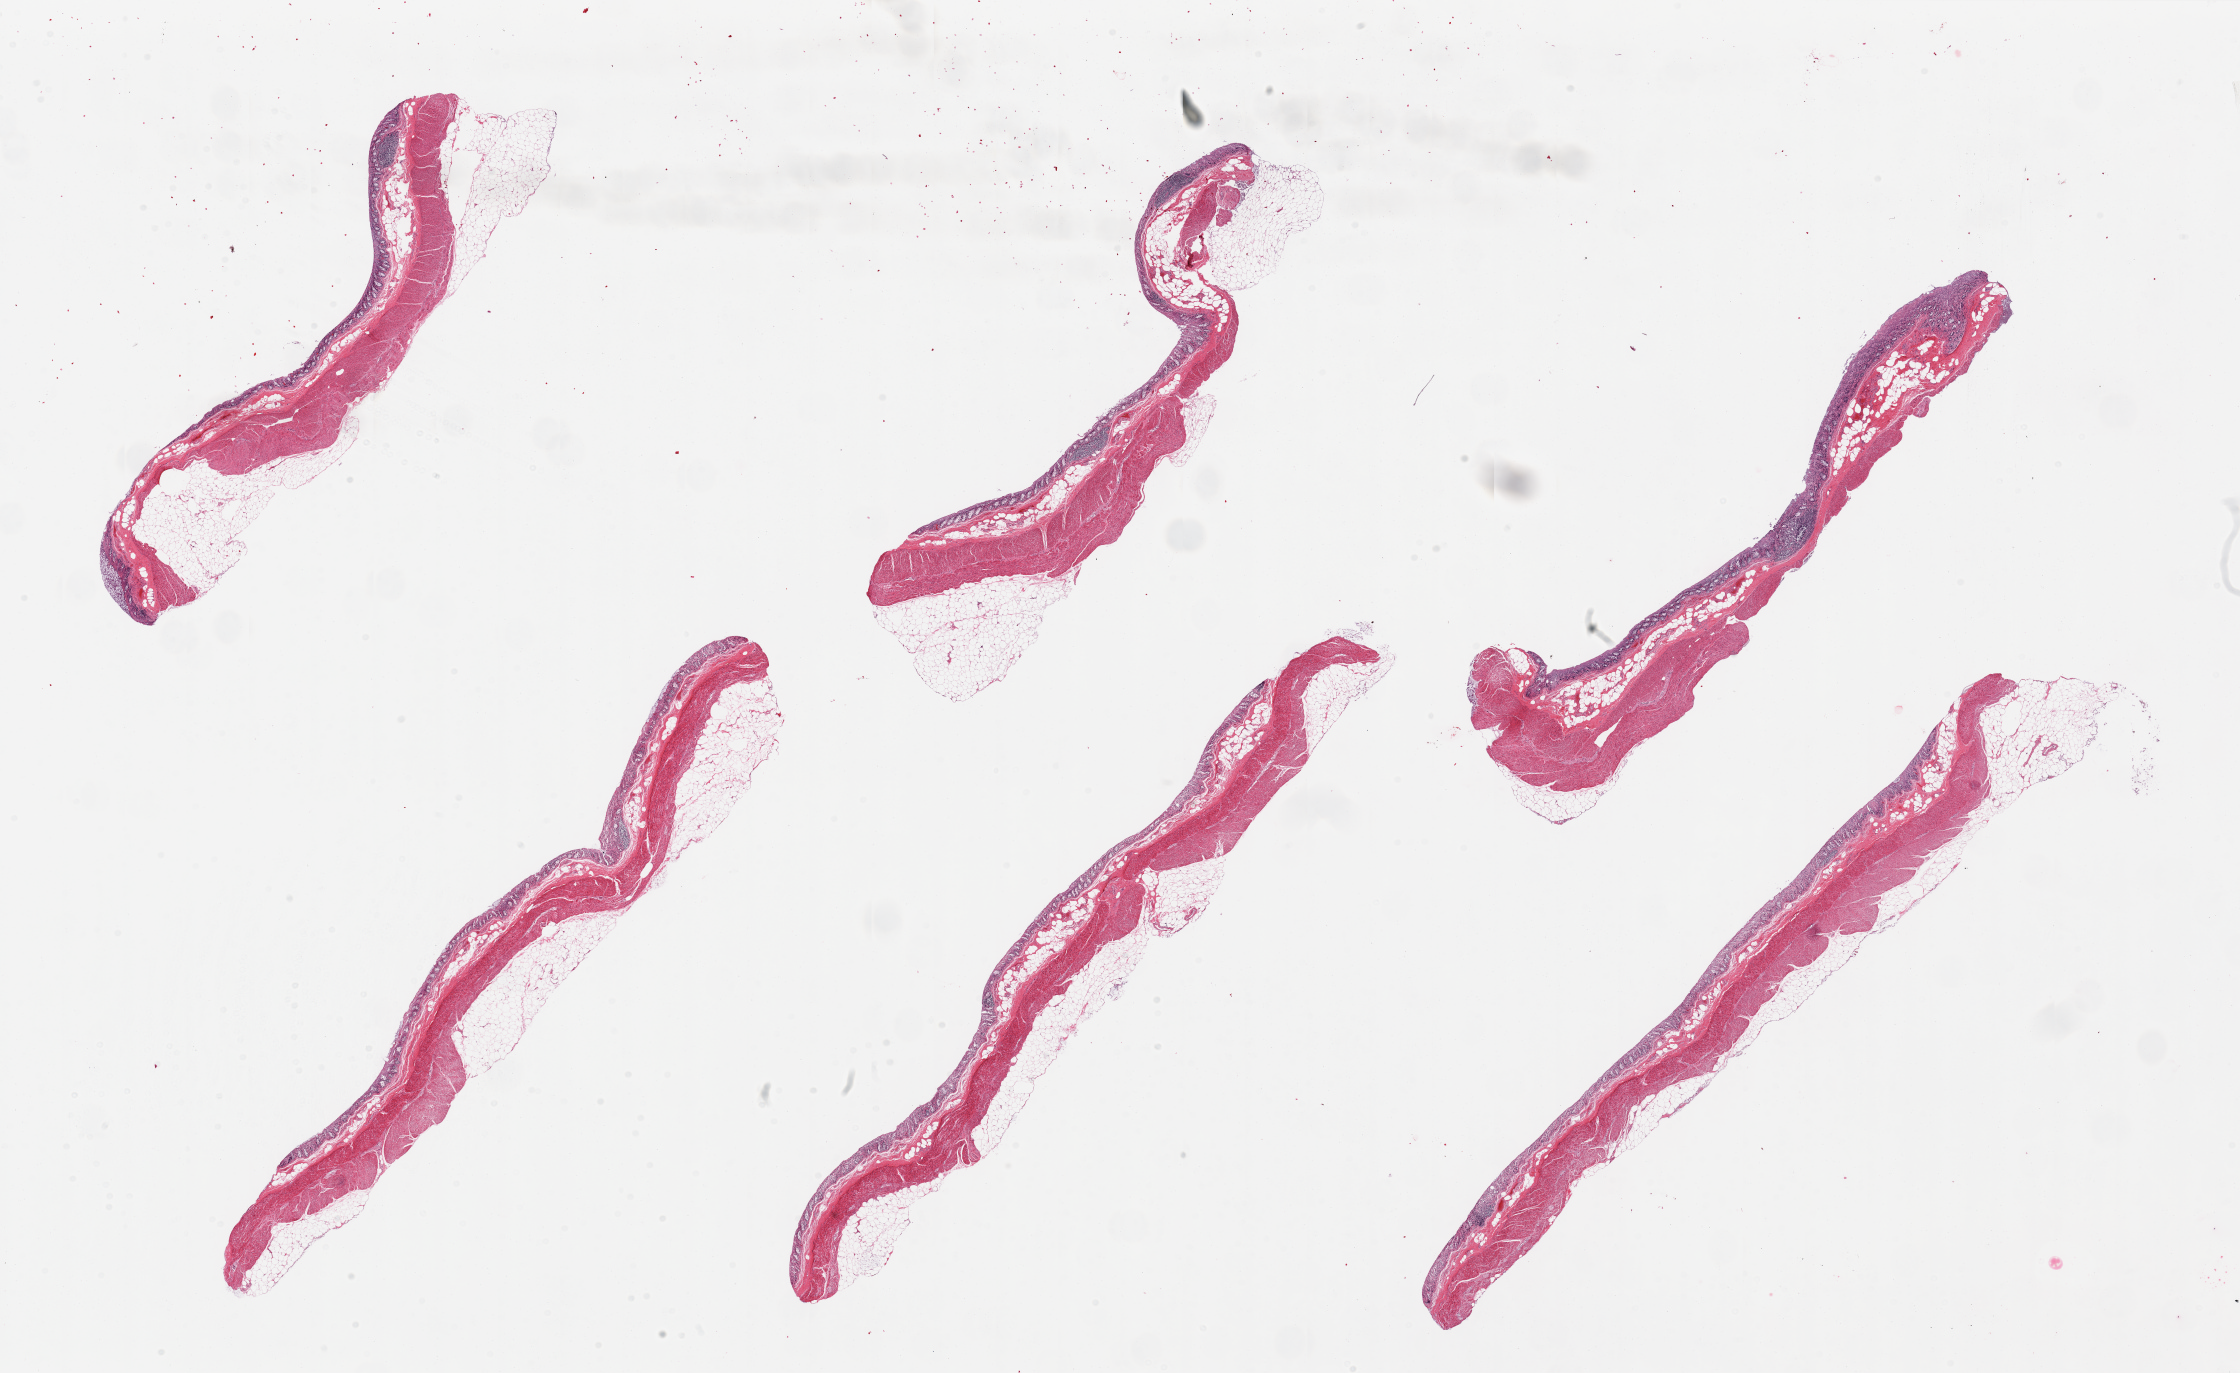
Whole-slide image, H&E stain, whole scanned area (about 35.4 x 21.7 mm) shown as a low-resolution overview; PAXgene-fixed paraffin-embedded (PFPE) section; target tissue: transverse colon; tissue donor sample. Donor sex: male.
Review note (as recorded): 6 pieces, severely autolyzed mucosa (3) and muscularis (1).